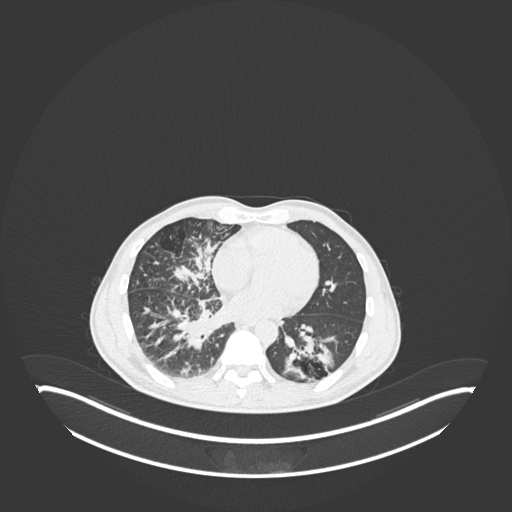
Chest CT, one axial slice; slice 96 of 237 in the series (ordered by position); reconstruction kernel B30f; 120 kVp; lung window (W 1500 / L -600 HU); 1 mm slice thickness; 512 × 512 image matrix, field of view 500 × 500 mm. Male patient, age 49 years. Case-level facts recorded for this patient, not image findings: clinical TNM (as recorded): T2b N1 M0.
Annotated regions visible in this slice (rectangle marked by the reading radiologist):
- lung tumour (recorded histology: adenocarcinoma): bounding box <283,327,338,379> (left, top, right, bottom; pixels)